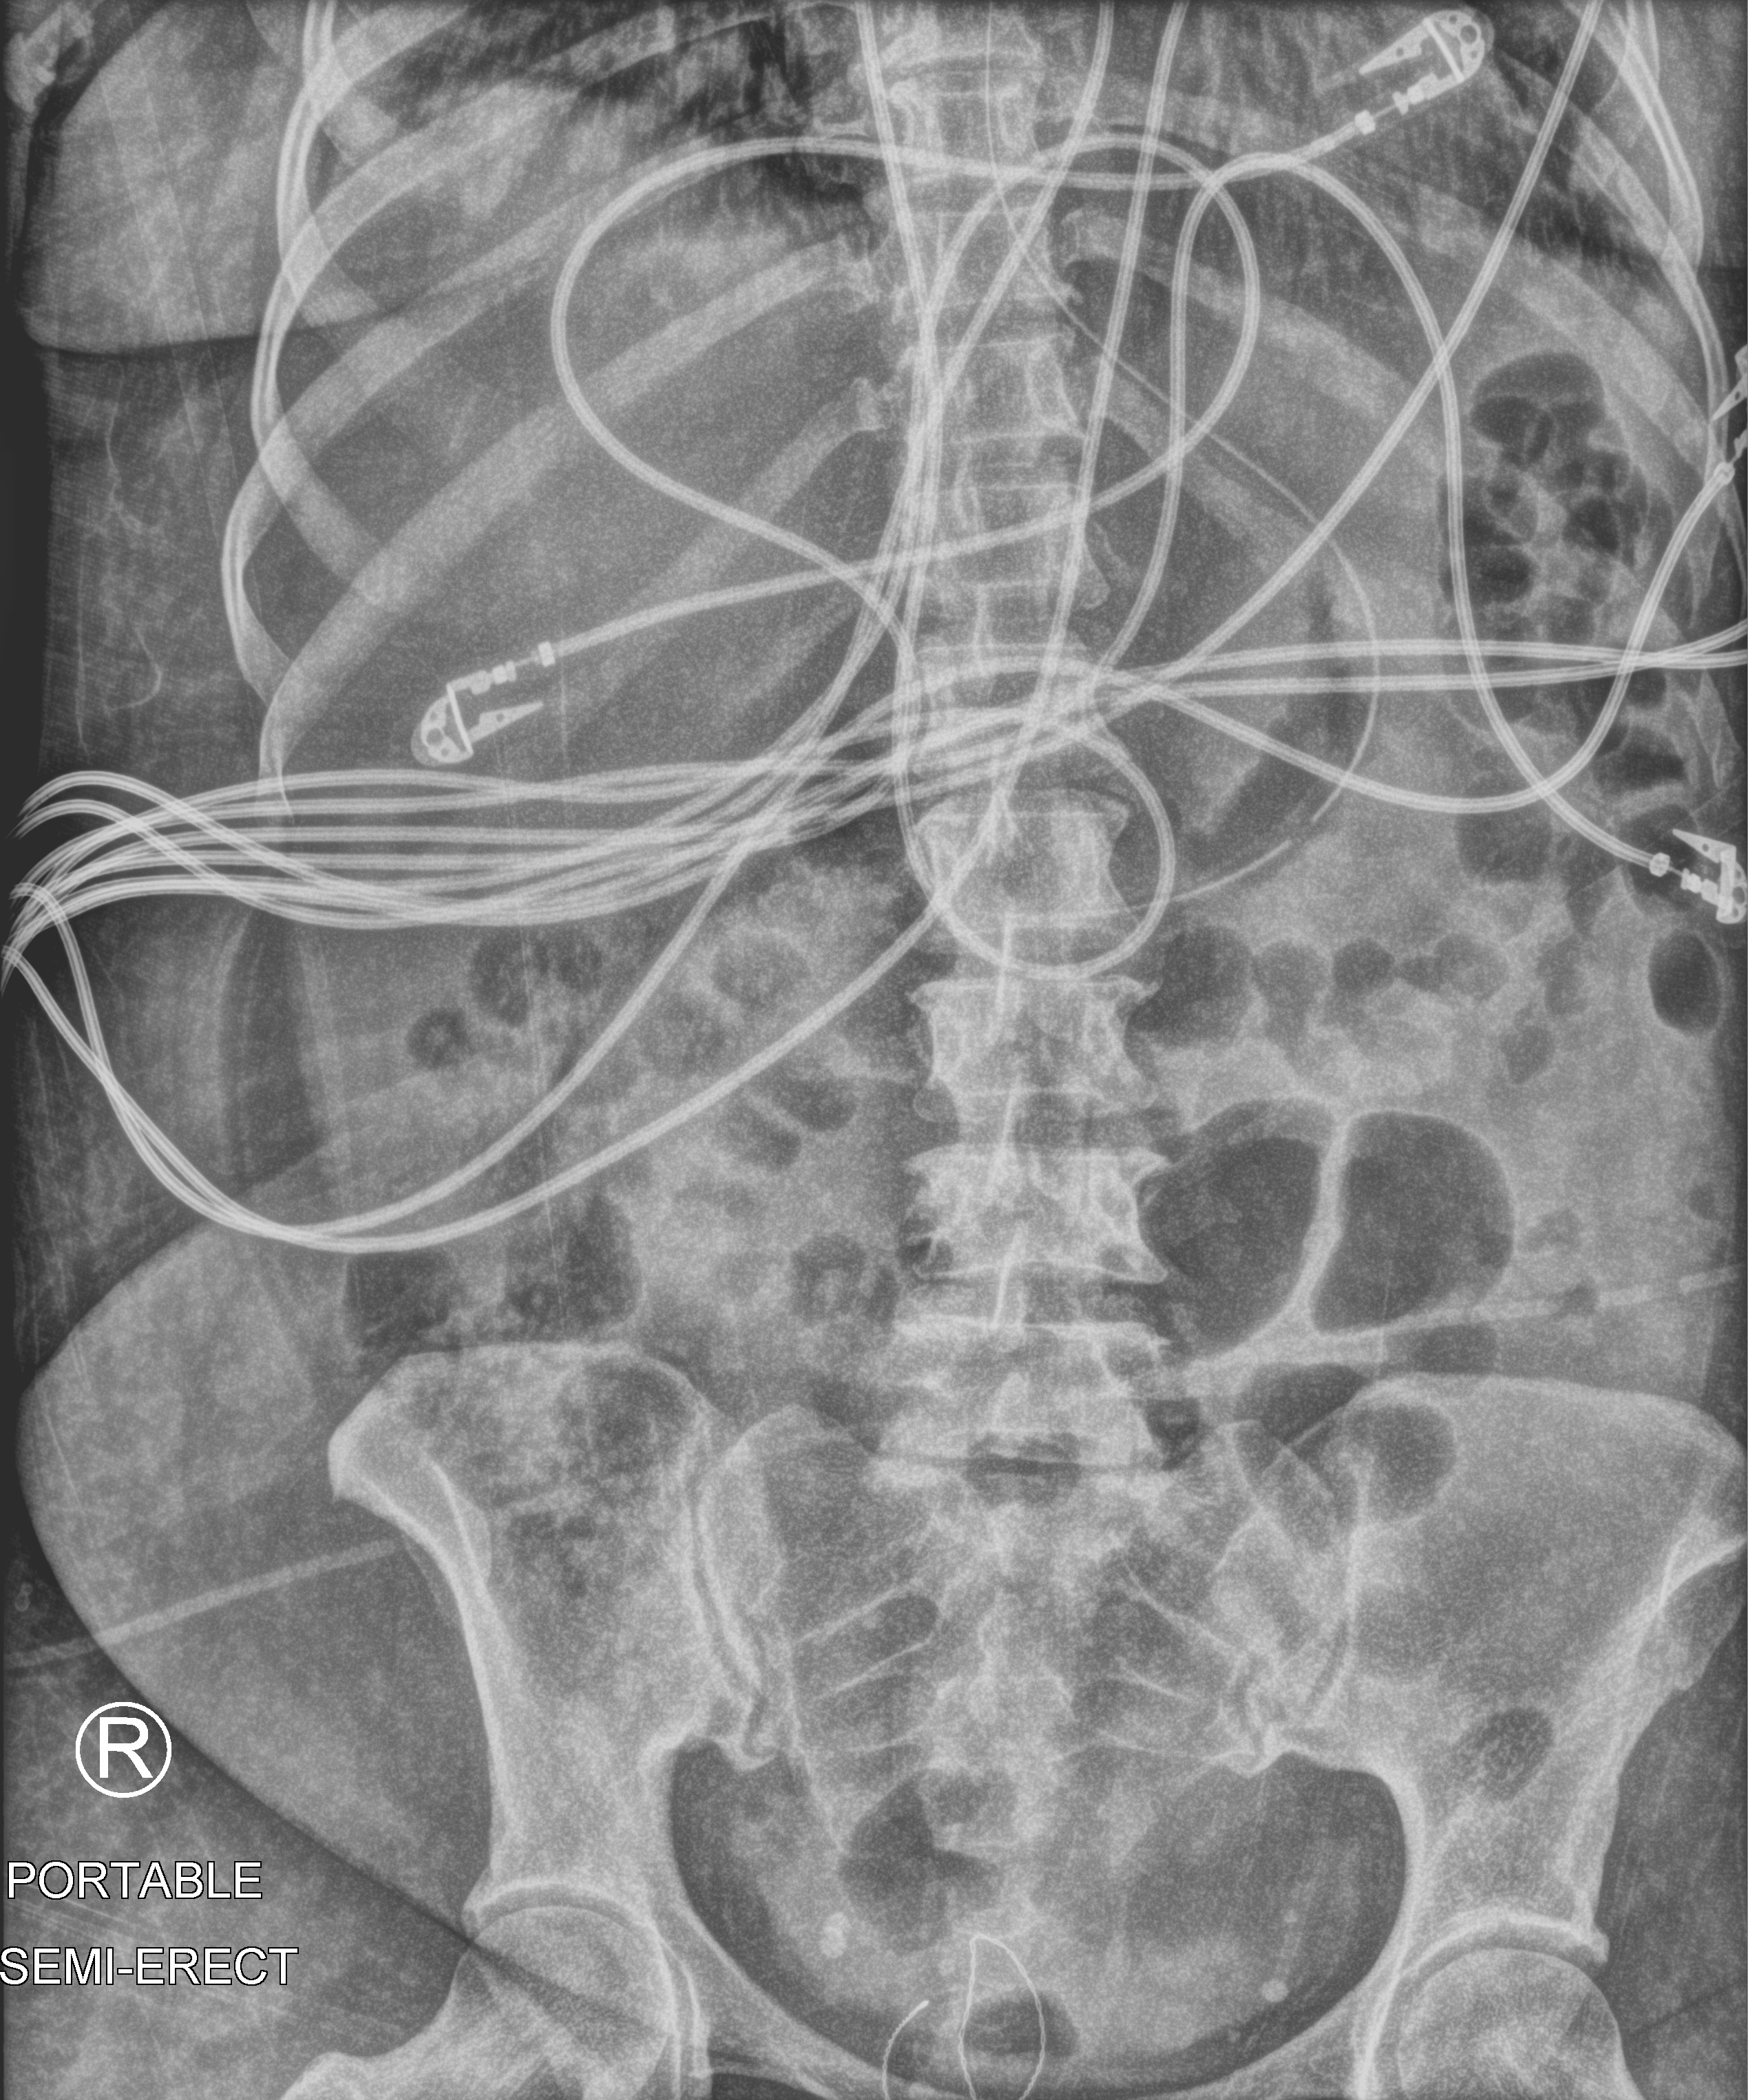
Portable abdomen radiograph, anteroposterior (AP) projection. Female patient hospitalised with COVID-19, age 18–59 years.
Admission-level facts for this patient (not findings on this image; timing relative to this image not recorded):
- mechanically ventilated during this hospital stay: yes
- length of hospital stay: 71 days